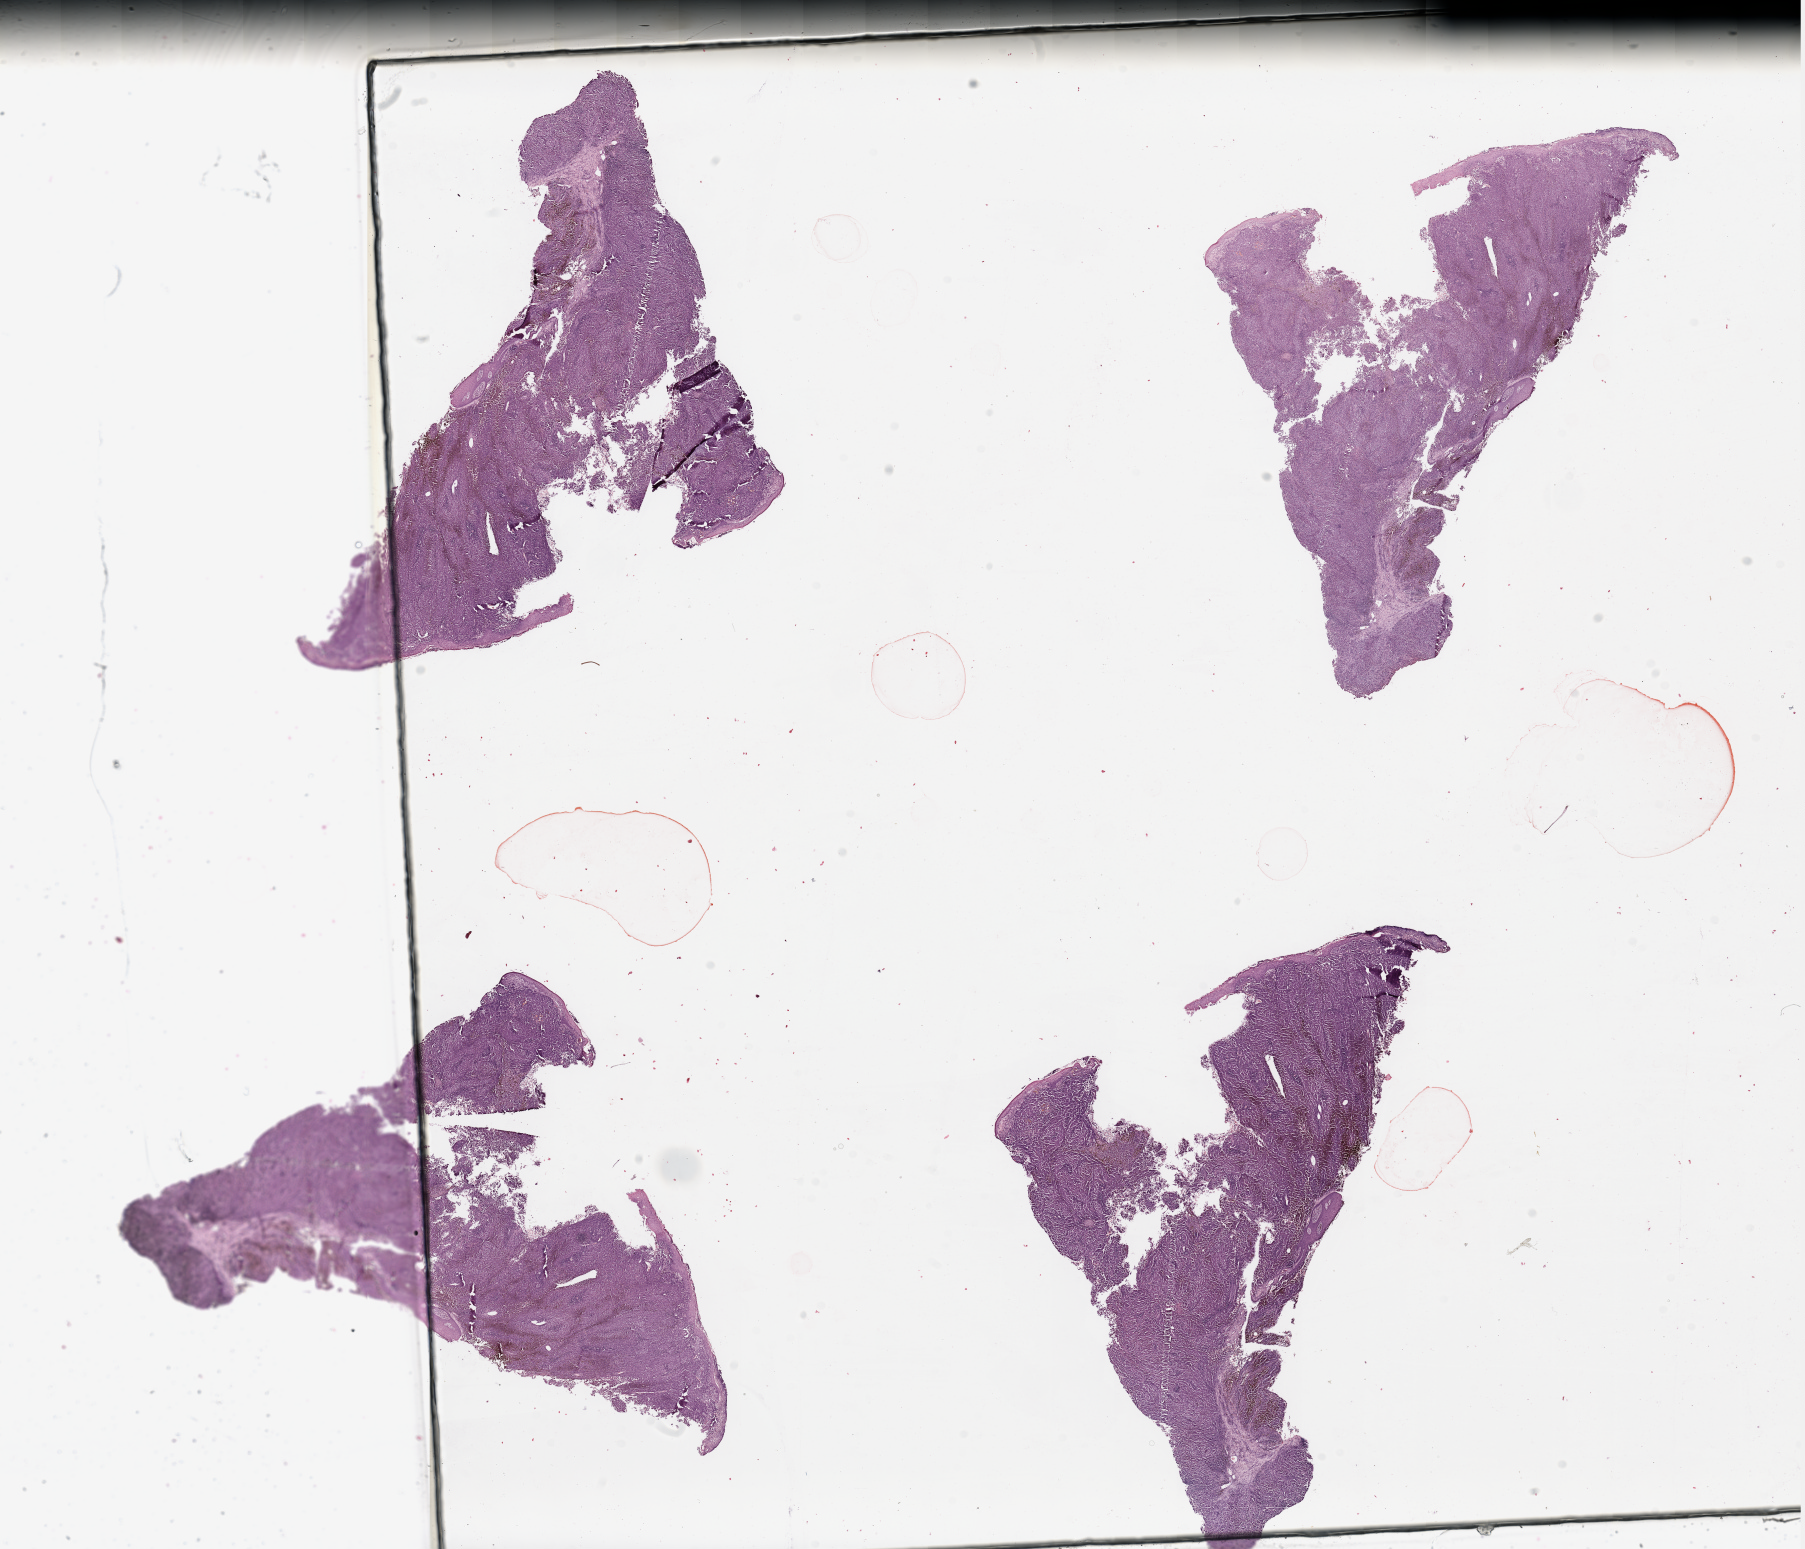
Digitized H&E-stained tissue section (whole slide), a low-resolution overview of the entire scanned area, about 28.5 x 24.5 mm (acquisition: 20x scan), melanoma tumour tissue; sampled site not recorded. Patient: male, age 60 years.
Histologic diagnosis: Malignant melanoma, NOS.